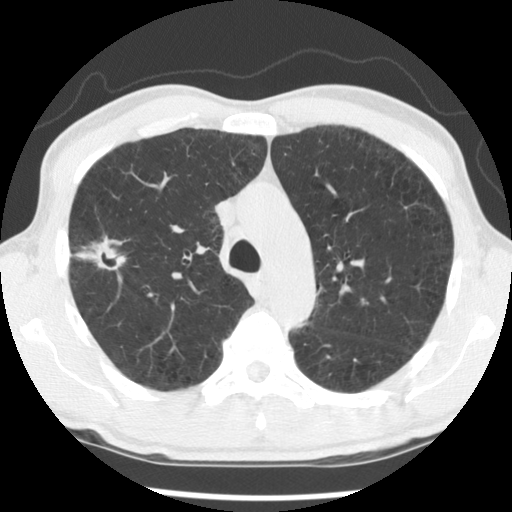
Low-dose screening chest CT, one axial slice. Position 92 of 138 along the scan axis. Reconstruction kernel STANDARD. 140 kVp. Lung window (W 1500 / L -600 HU). 2.5 mm slice thickness. 512 × 512 image matrix.
Annotated regions visible in this slice (expert manual segmentation):
- lesion 1 (tumor, upper lobe of right lung): box from (x=76, y=236) to (x=126, y=270) px